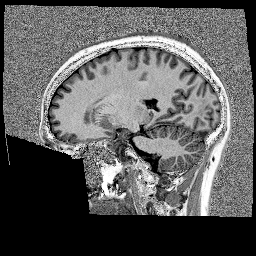
Brain MRI from a brain-tumour surgery series, one sagittal slice; slice 73 of 176 in the series (ordered by position); 1 mm slice thickness; 256 × 256 image matrix, field of view 256 × 256 mm. From the clinical record (not read from this slice): histopathology: Glioblastoma; WHO grade: 4; IDH mutation: no.
Outlined on this slice (expert manual segmentation):
- tumour: bounding box <138,69,144,76> (left, top, right, bottom; pixels)